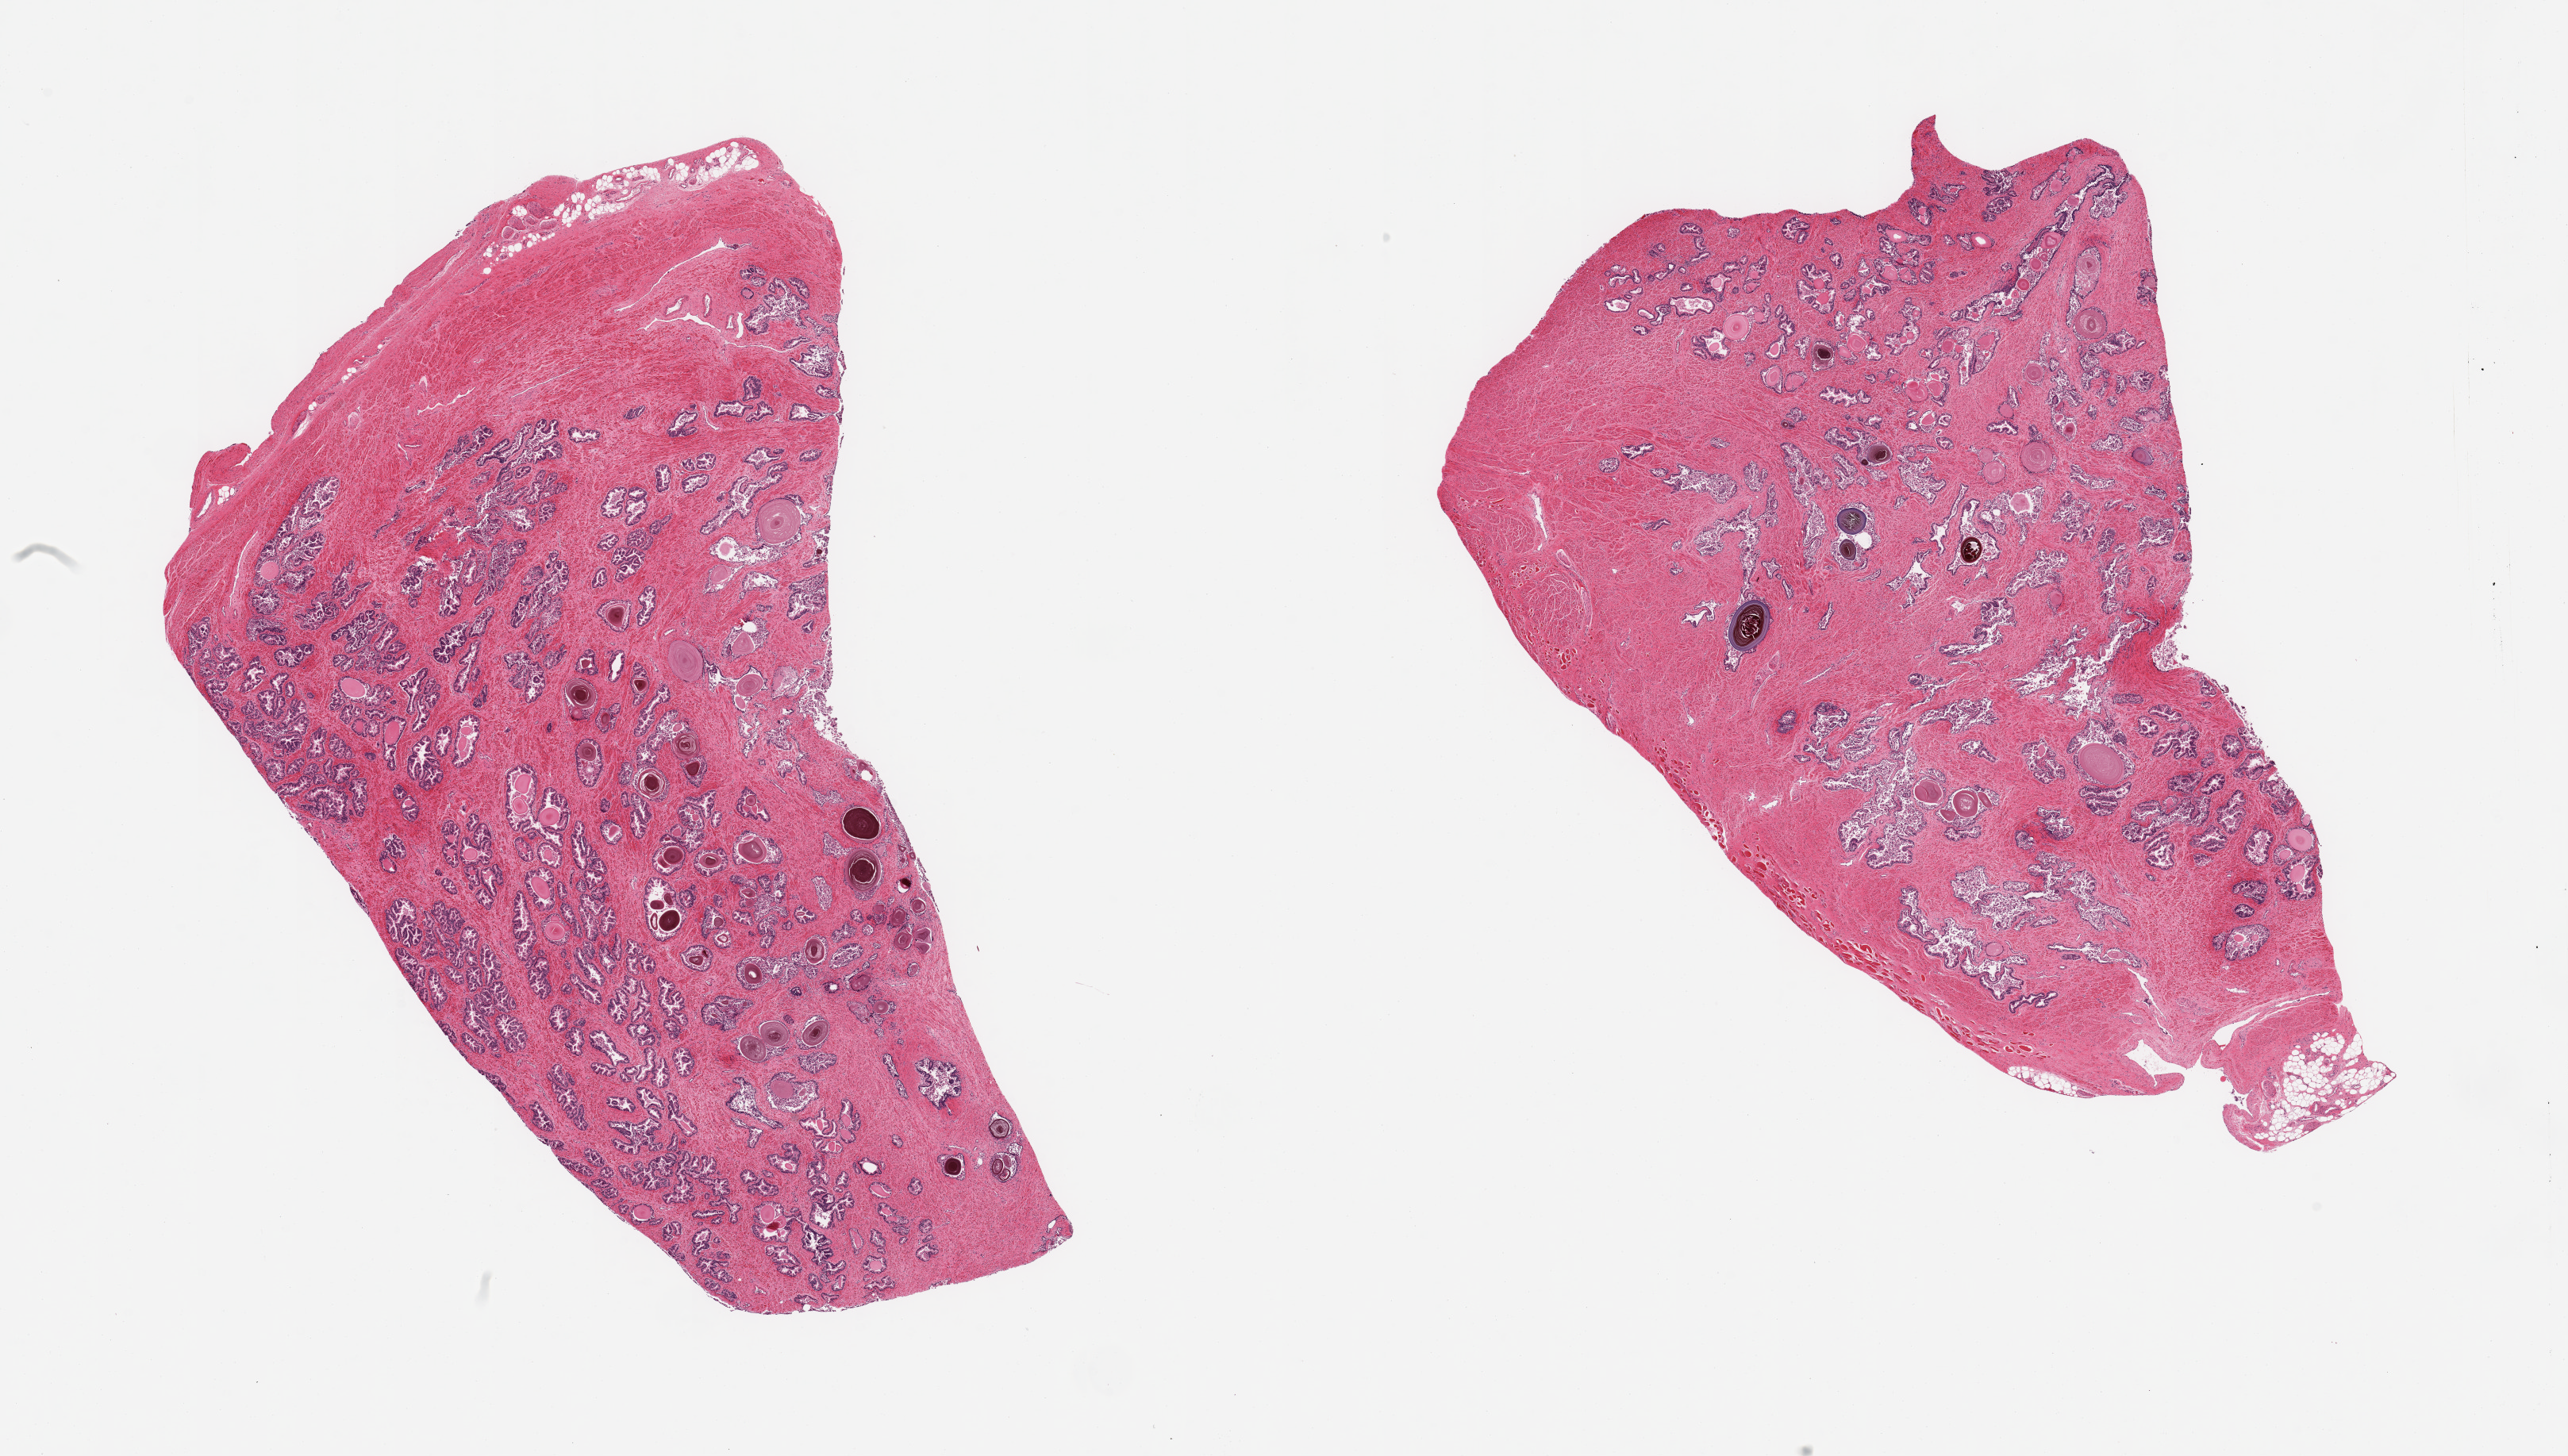
Digitized haematoxylin and eosin-stained section — a low-resolution overview of the entire scanned area, about 25.6 x 14.5 mm (acquisition: 20x scan). PAXgene-fixed paraffin-embedded (PFPE) section. Section of prostate (target tissue). Tissue donor sample.
Reviewer comment on this tissue sample: 2 pieces; mild to moderated autolysis; fibromuscular stroma and glandular componenet with corpora amylacea and sloughed glandular epithelium.